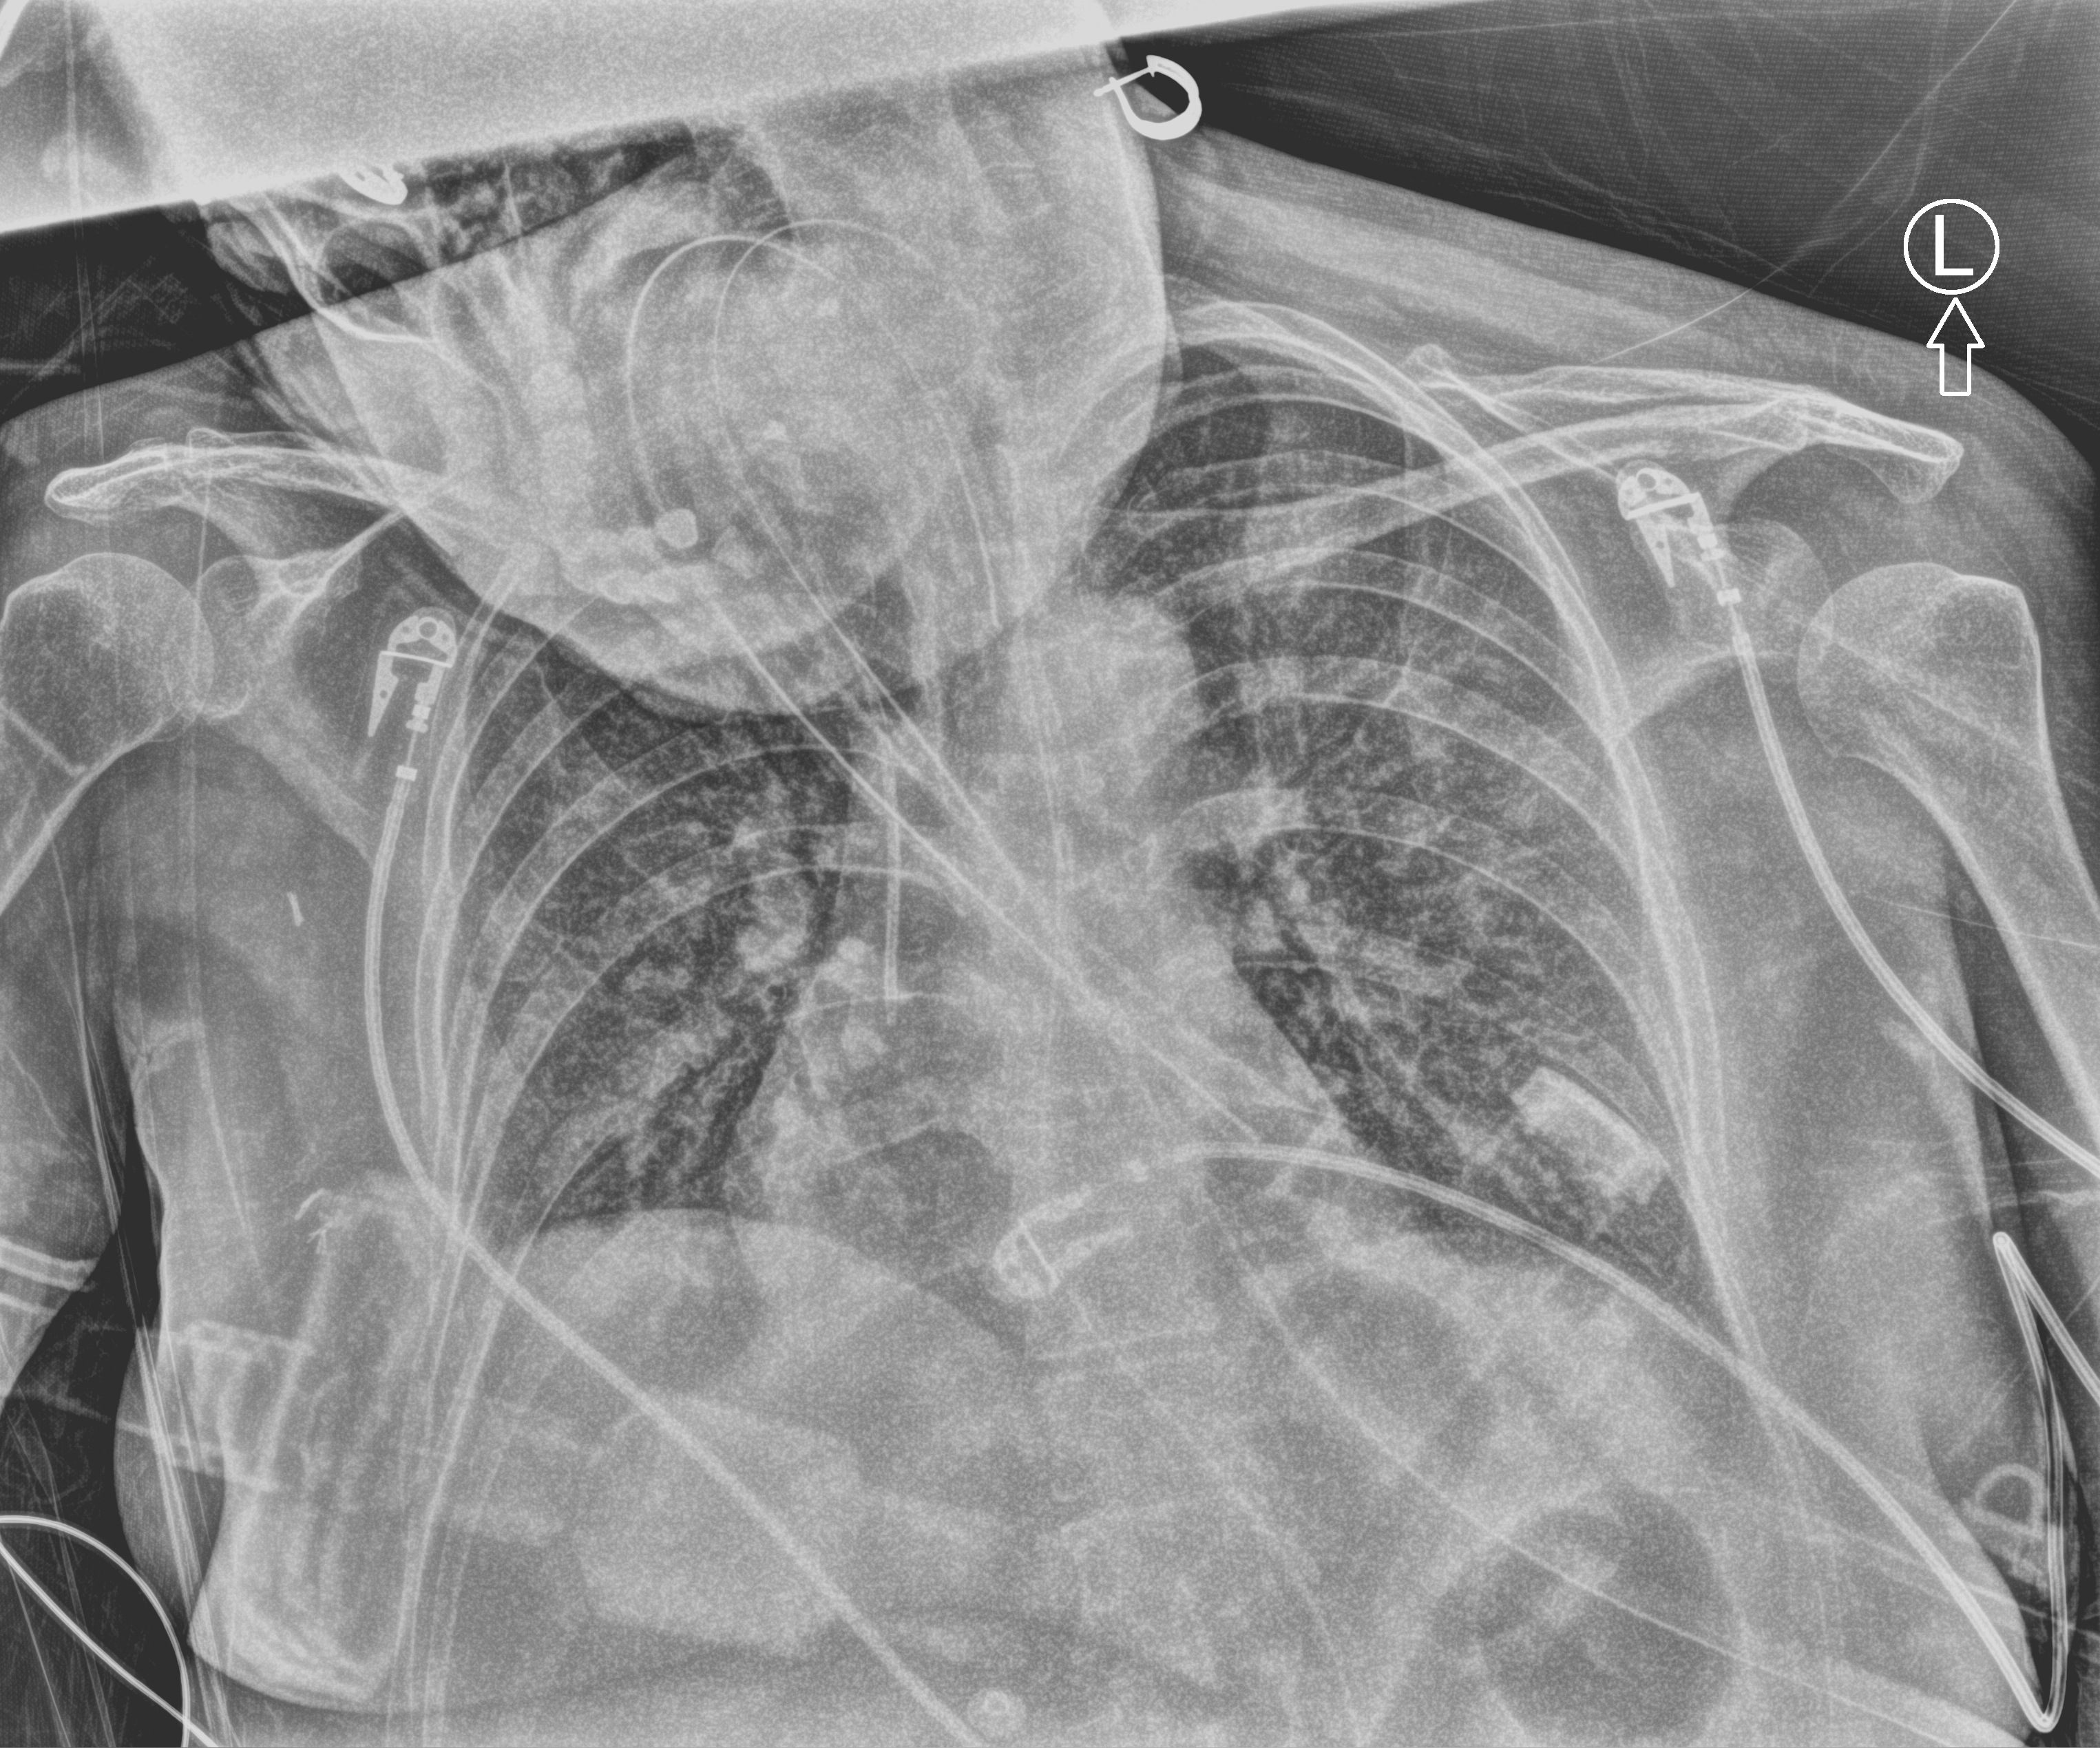
Chest X-ray (portable). Female patient hospitalised with COVID-19, age 18–59 years.
Hospital-stay facts (about this admission, not read from this image; timing relative to this image not recorded):
- length of hospital stay: 21 days
- mechanically ventilated during this hospital stay: yes